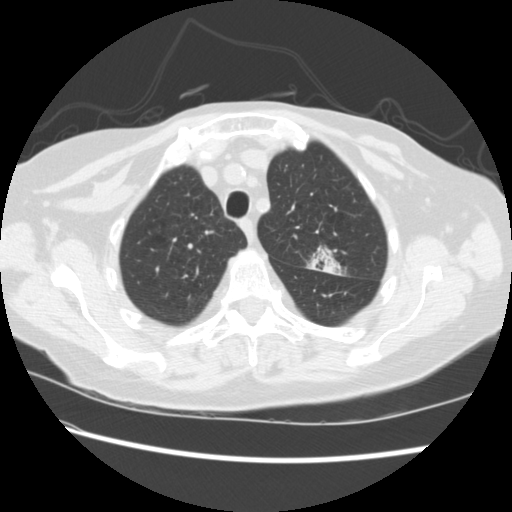
Low-dose screening chest CT, one axial slice. Slice 175 of 224 in the series (ordered by position). Reconstruction kernel STANDARD. Lung window (W 1500 / L -600 HU). 2.5 mm slice thickness. 512 × 512 image matrix, field of view 340 × 340 mm.
Outlined on this slice (manually delineated by an expert):
- lesion 1 (tumor, upper lobe of left lung): bounding box (x1, y1, x2, y2) in pixels: (307, 247, 342, 275)